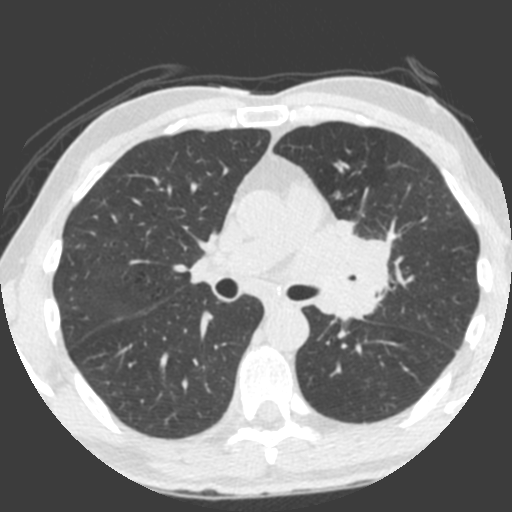
Low-dose screening chest CT, one axial slice; slice 132 of 212 in the series (ordered by position); 120 kVp; lung window (W 1500 / L -600 HU); 512 × 512 image matrix, field of view 315 × 315 mm.
Structures marked on this image (outlined manually by an expert reader):
- lesion 1 (tumor, upper lobe of left lung): box from (x=315, y=220) to (x=392, y=320) px